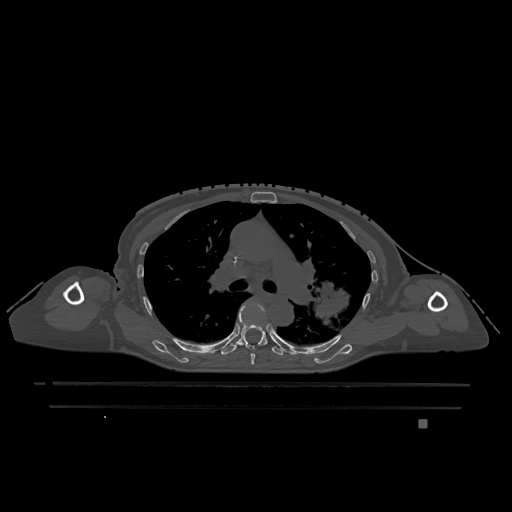
CT including the spine, one axial slice. Position 808 of 1317 along the scan axis. Bone window (W 1800 / L 400 HU). 0.5 mm slice thickness. 512 × 512 image matrix, field of view 500 × 500 mm. Female patient, age 74 years. From the clinical record (not read from this slice): primary cancer: lung; vertebrae with lytic lesions (as recorded): T1, T4, T5, T6, L4, L5.
Annotated regions visible in this slice (semi-automatically segmented with operator editing):
- T5 vertebra: bounding box [x1, y1, x2, y2] px = [250, 304, 265, 365]
- T6 vertebra: [221, 306, 283, 355]